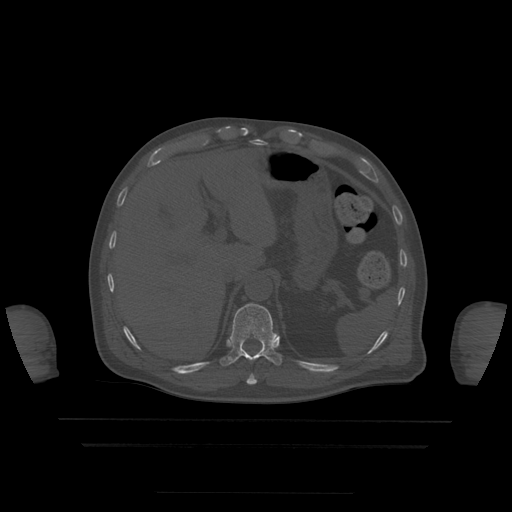
CT including the spine, one axial slice; position 223 of 522 along the scan axis; bone window (W 1800 / L 400 HU); 512 × 512 image matrix, field of view 436 × 436 mm. Patient age 68 years. Case-level facts recorded for this patient, not image findings: primary cancer: urothelial.
Outlined on this slice (semi-automatically segmented with operator editing):
- T10 vertebra: box from (x=247, y=374) to (x=257, y=385) px
- T11 vertebra: (x=220, y=304)–(x=282, y=367)